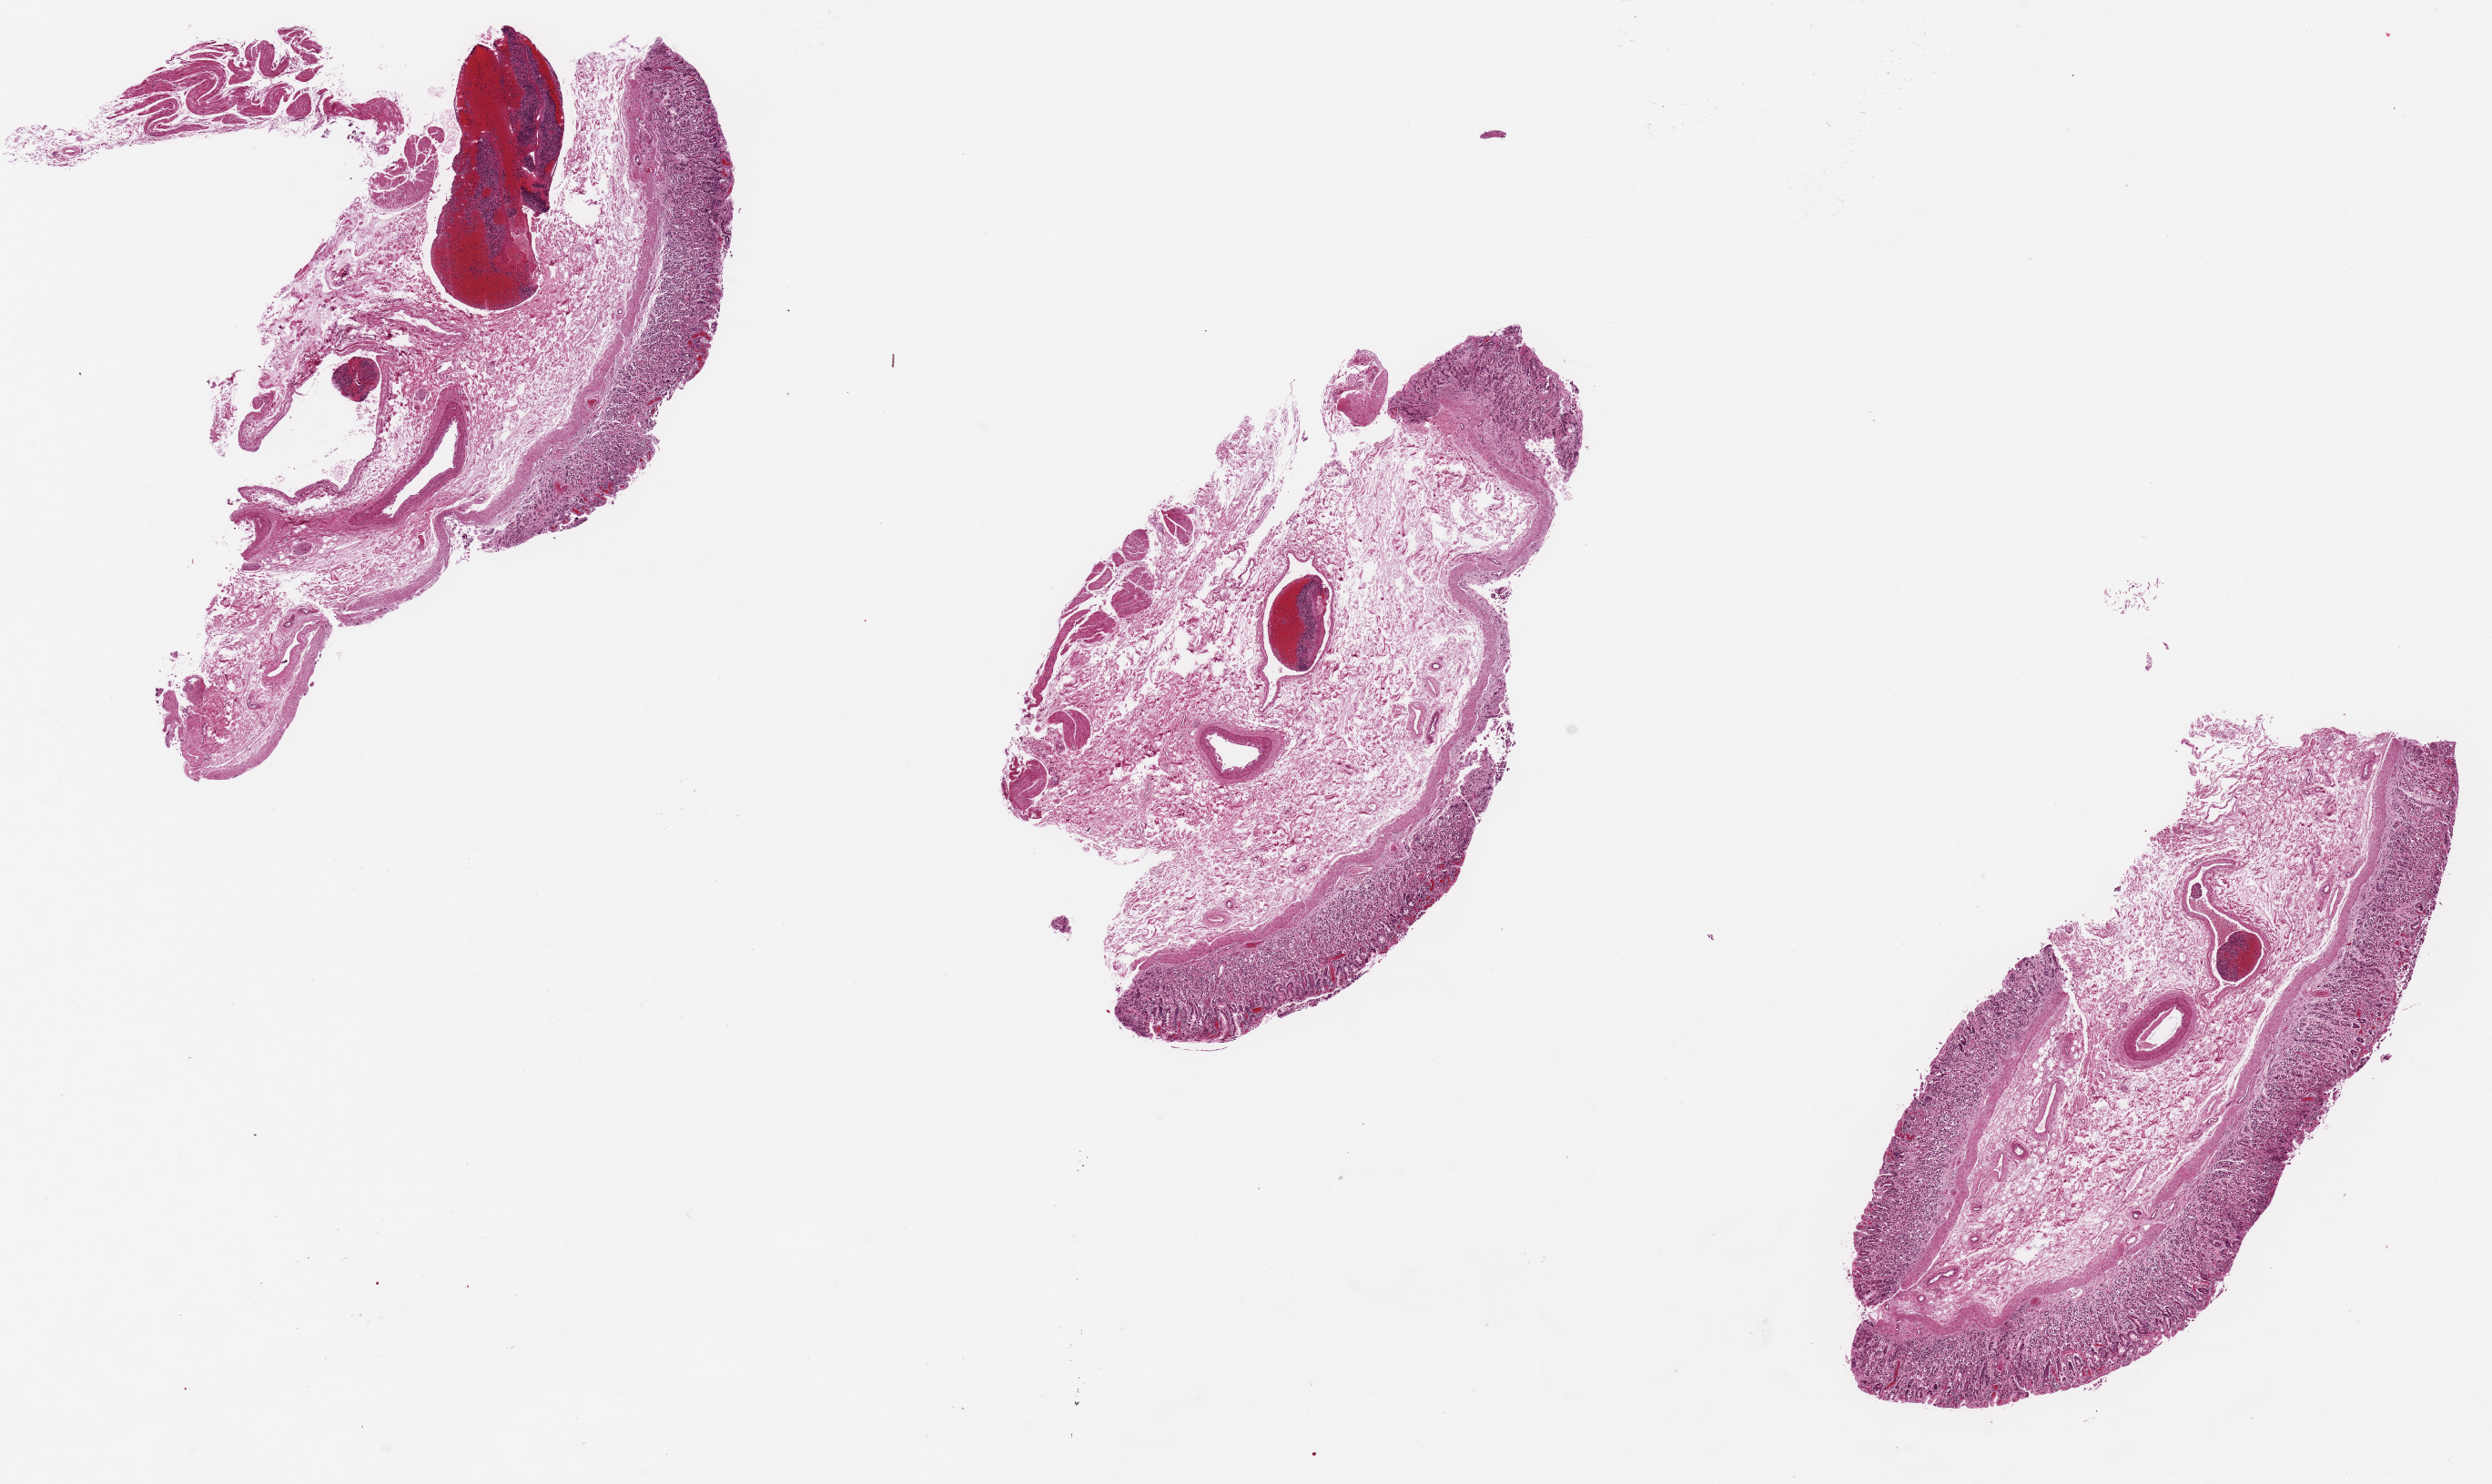
Whole-slide image, hematoxylin and eosin (H&E) stain, whole scanned area (about 21.7 x 12.9 mm) shown as a low-resolution overview, PAXgene-fixed, paraffin-embedded tissue, target tissue: transverse colon, donor tissue sample. Female donor.
Review note (as recorded): Mucosa is ~15--30% of specimen thickness where present; 40-50% is sloughed.